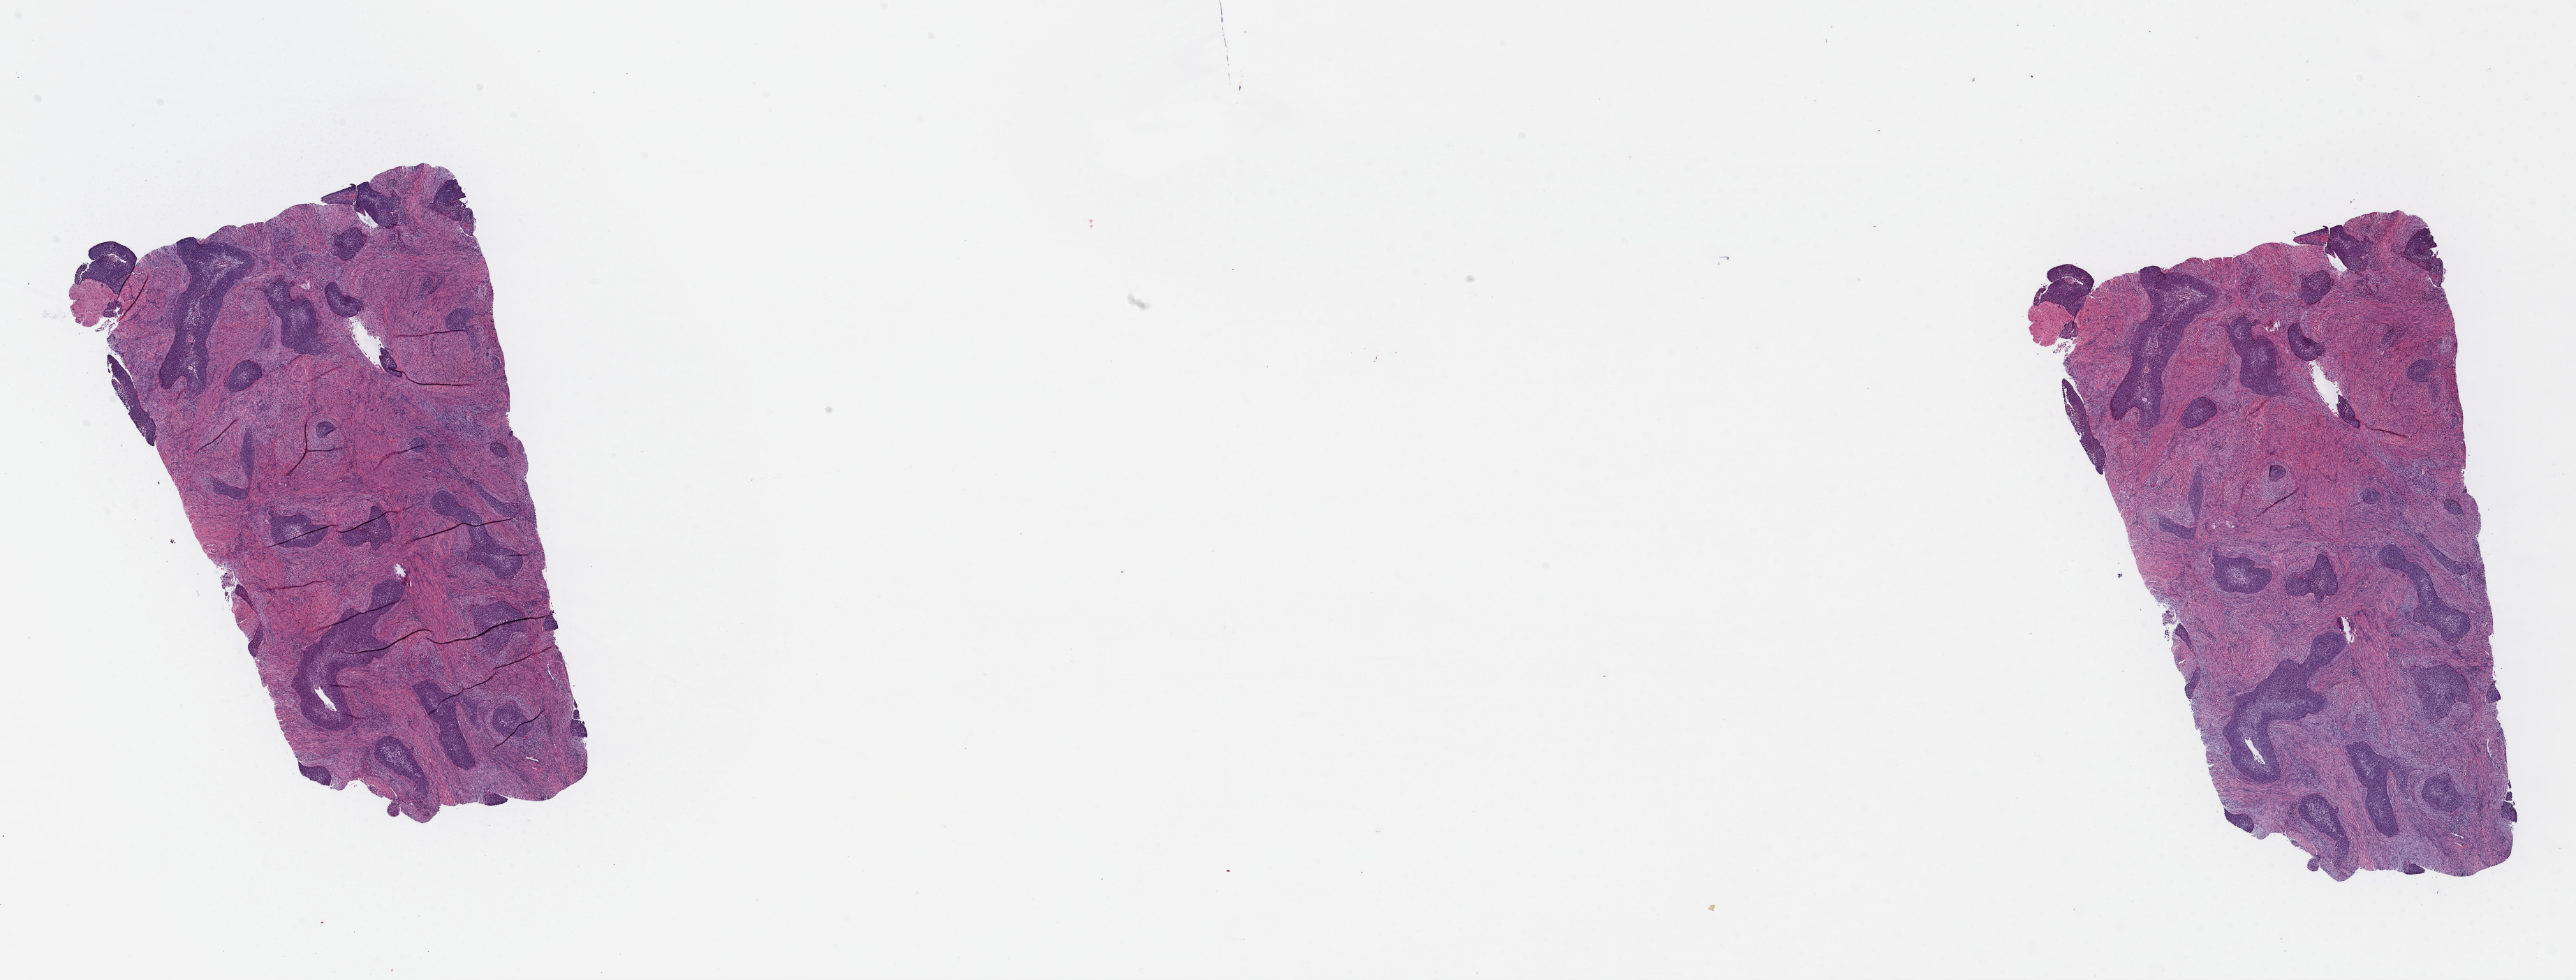
Digitized H&E tissue section (whole slide), shown as a low-resolution overview of the whole scanned area (about 29.0 x 11.0 mm, acquisition: 40x scan), formalin-fixed paraffin-embedded (FFPE) diagnostic section, cervix, primary tumour sample. Patient: female, age at initial diagnosis 64 years. Histologic grade: G3 (poorly differentiated).
Pathologic diagnosis: Squamous cell carcinoma, NOS (cervix uteri). FIGO stage: IIA2.